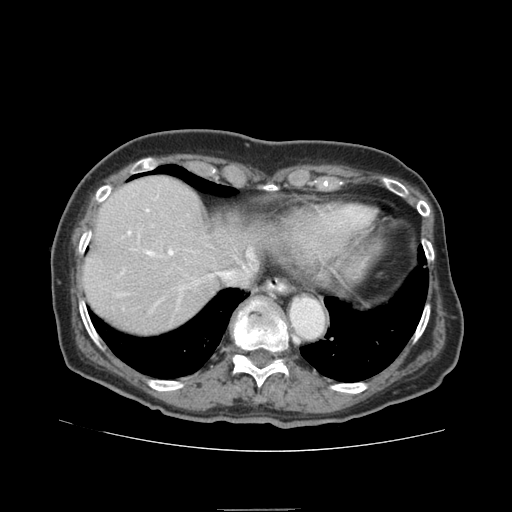
Contrast-enhanced abdominal CT (liver protocol), one axial slice; position 69 of 95 along the scan axis; reconstruction kernel STANDARD; soft-tissue window (W 400 / L 40 HU); 512 × 512 image matrix, field of view 360 × 360 mm. Case-level facts recorded for this patient, not image findings: diagnosis: hepatocellular carcinoma (patient treated with transarterial chemoembolisation; whether this scan precedes or follows treatment is not stated here); TNM stage (as recorded): Stage-IVA; Child-Pugh class: B; tumour differentiation: moderately differentiated.
Annotated regions visible in this slice (semi-automatically segmented with operator editing):
- liver parenchyma outside the tumour (the mass and vessels are separate outlines, so this box may not span the whole liver): bounding box (x1, y1, x2, y2) in pixels: (82, 176, 264, 332)
- liver vessels: (127, 209, 252, 277)